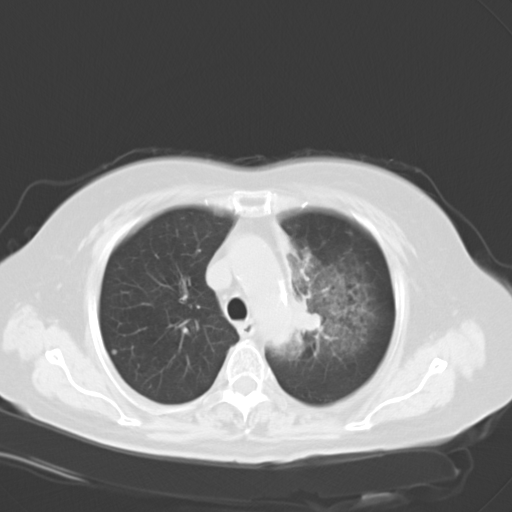
Chest CT, one axial slice. Position 21 of 28 along the scan axis. Reconstruction kernel B40f. Lung window (W 1500 / L -600 HU). 512 × 512 image matrix, field of view 353 × 353 mm. Patient: female, 65 years. Case-level facts recorded for this patient, not image findings: clinical TNM (as recorded): T2b N1 M0.
Annotated regions visible in this slice (rectangle marked by the reading radiologist):
- lung tumour (recorded histology: adenocarcinoma): bounding box <293,294,324,339> (left, top, right, bottom; pixels)